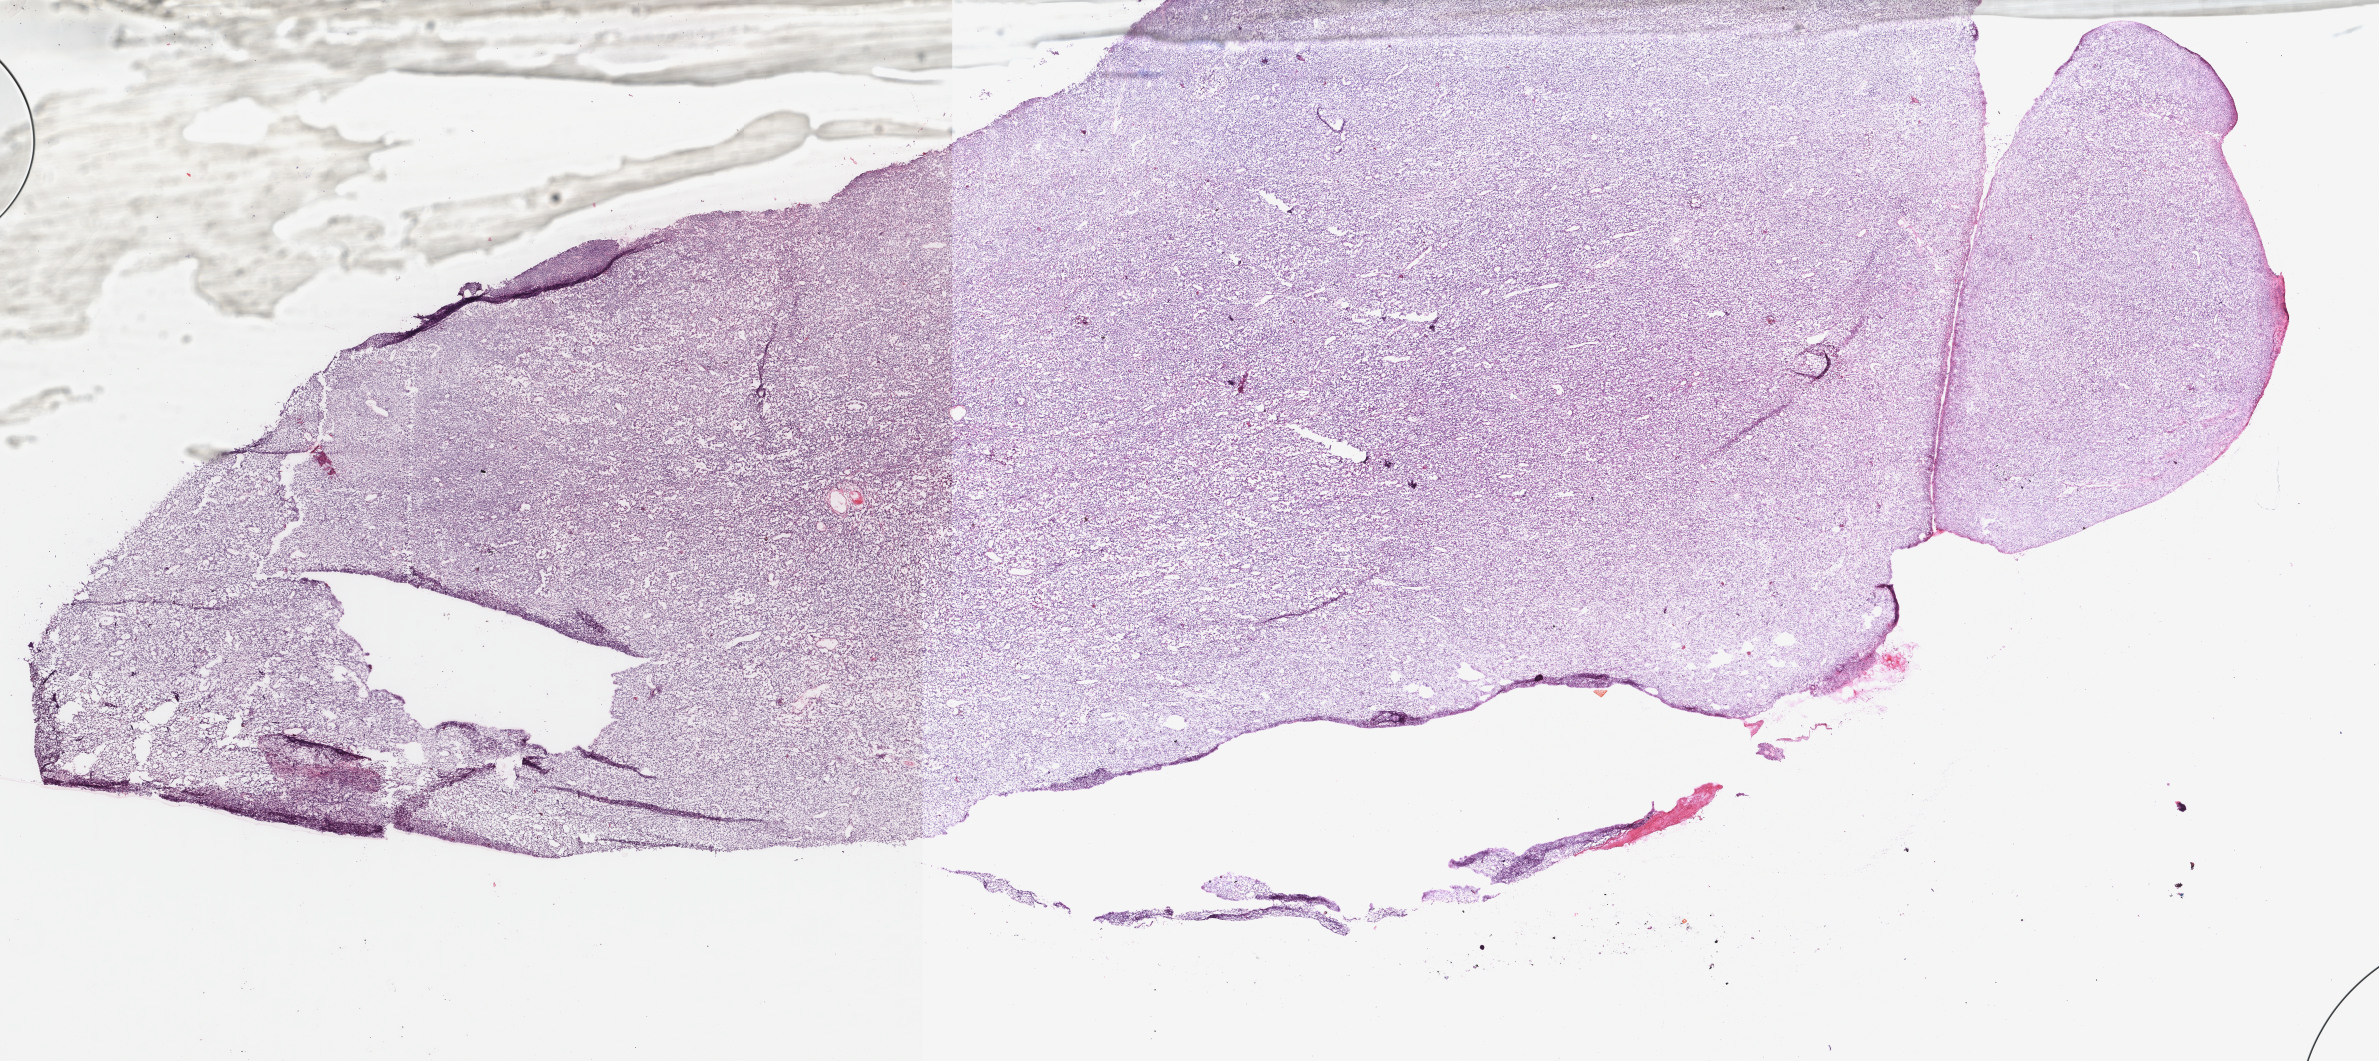
Digitized H&E tissue section (whole slide), a low-resolution overview of the entire scanned area, about 18.9 x 8.4 mm, formalin-fixed paraffin-embedded (FFPE) diagnostic section, primary tumour sample from the skin. Patient: male, age at initial diagnosis 25 years.
Histologic diagnosis: Malignant melanoma, NOS.